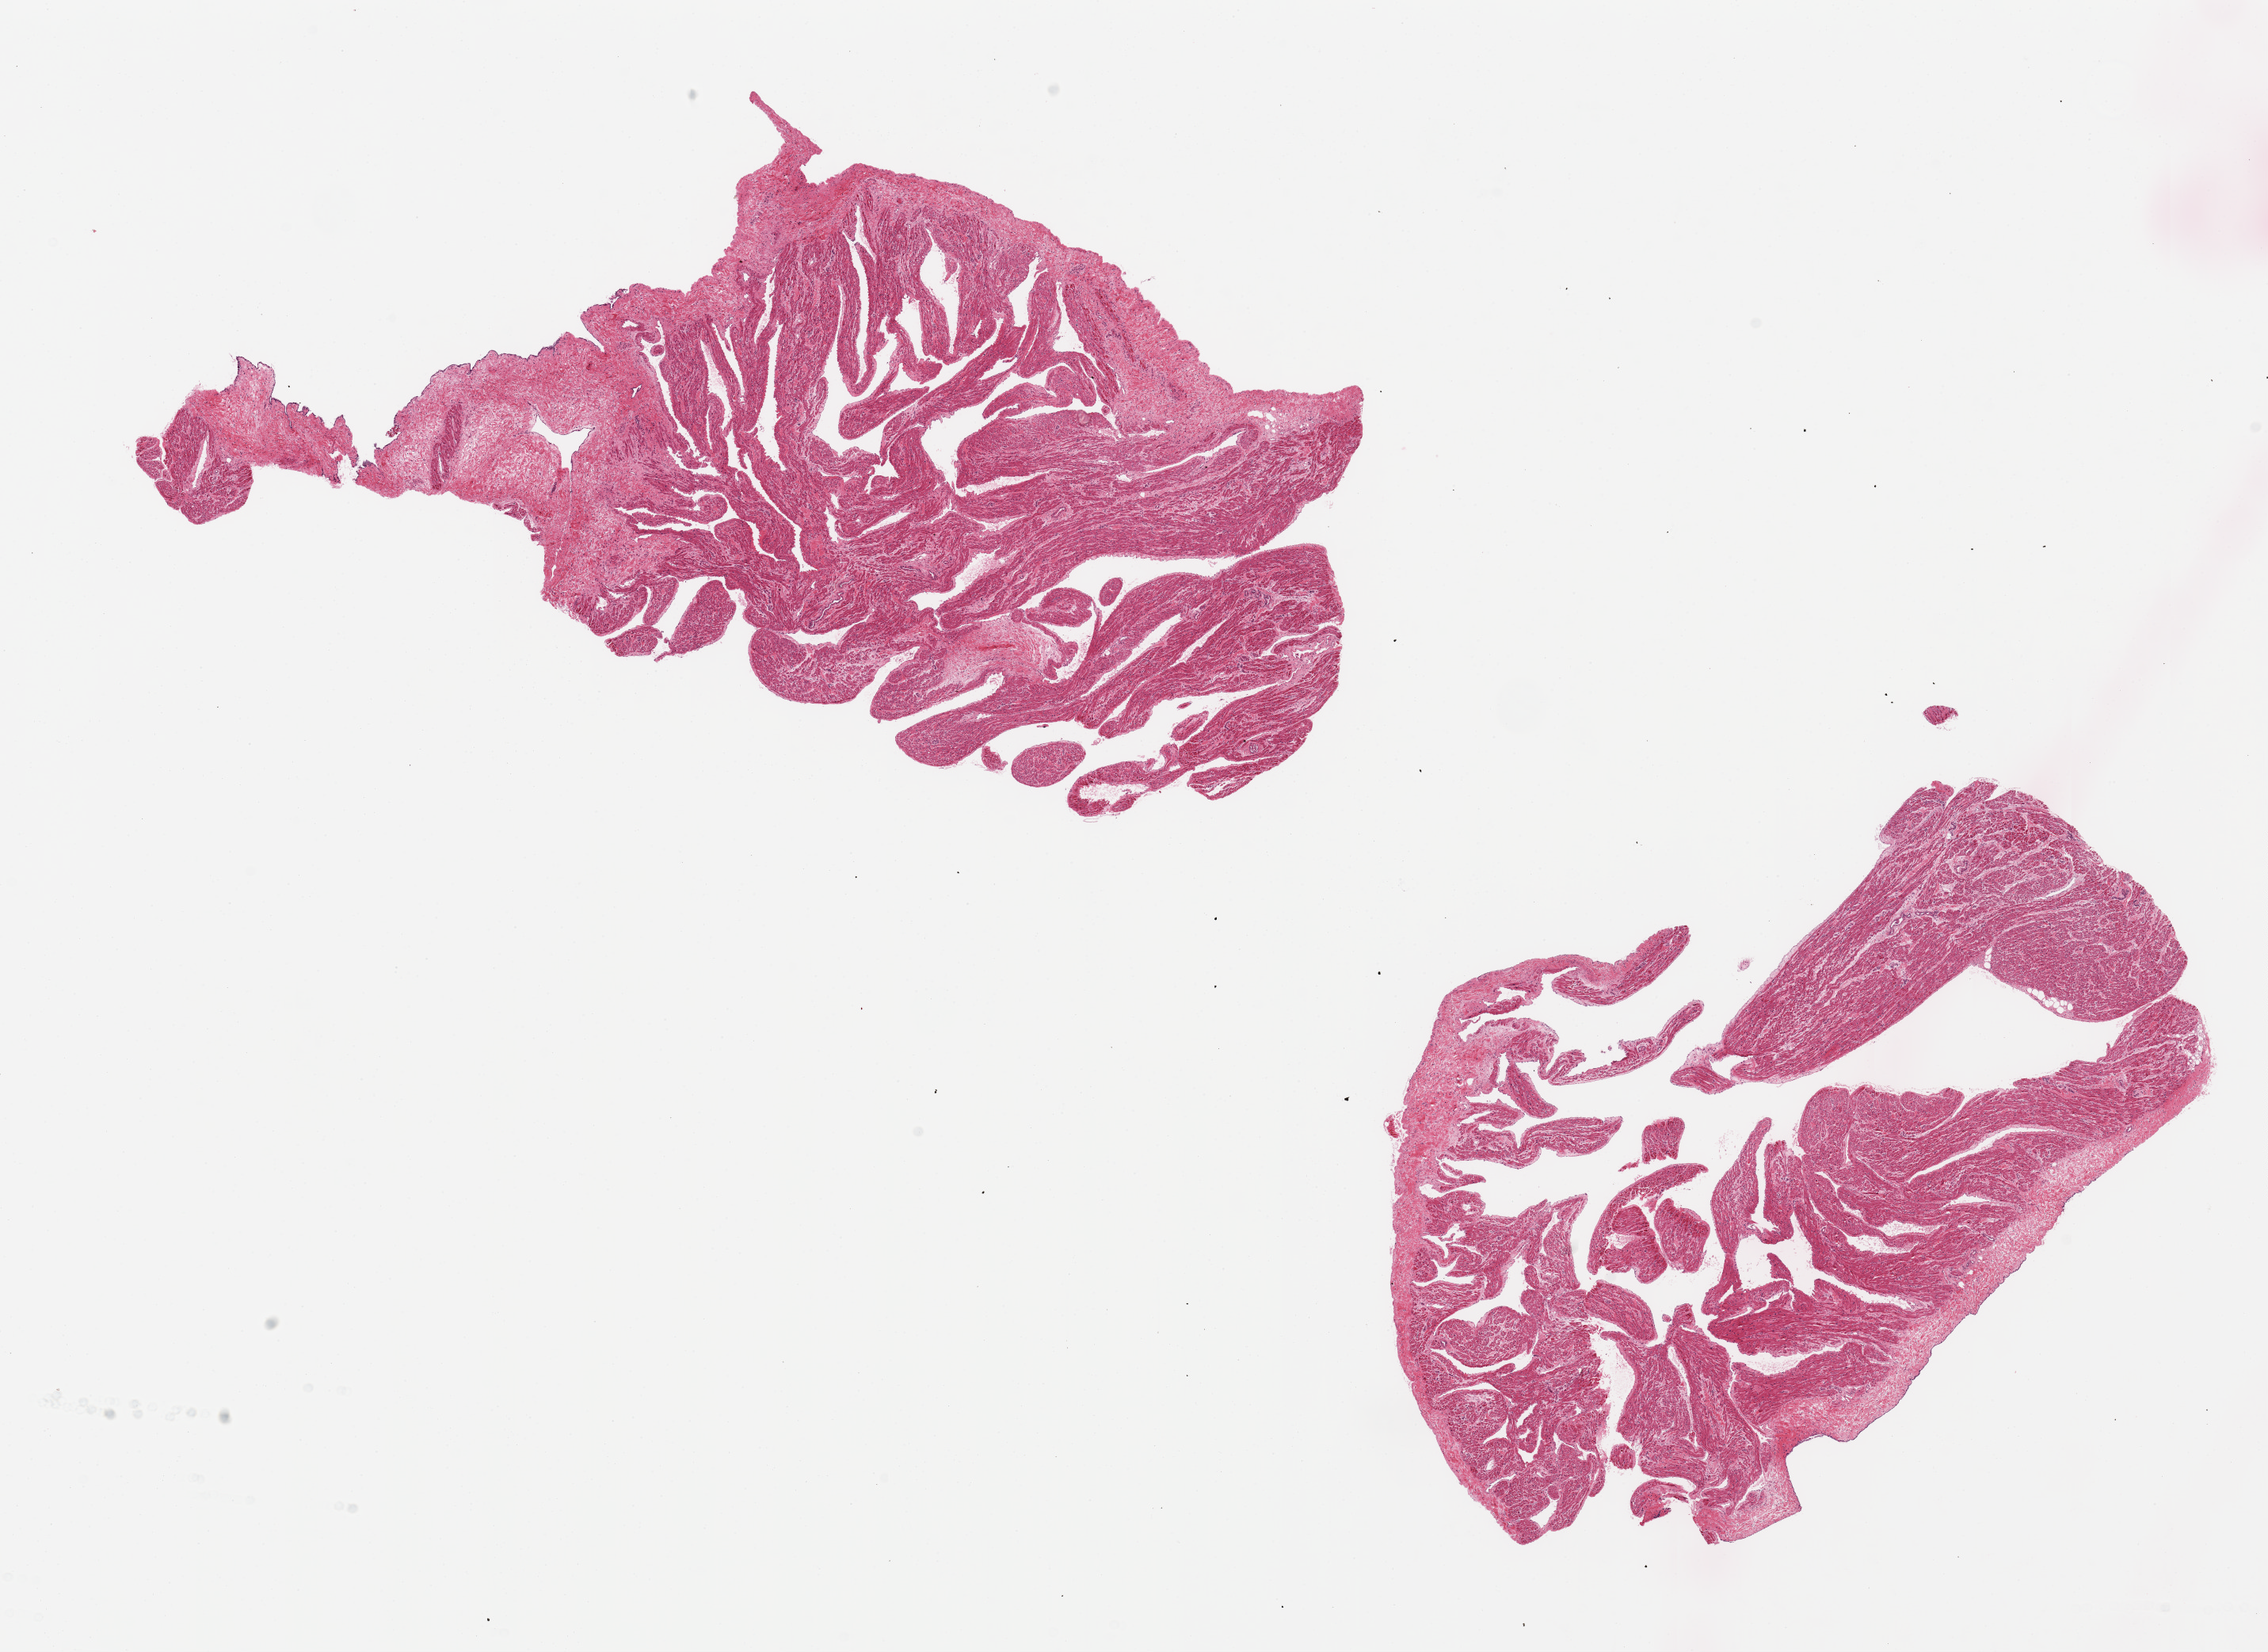
Hematoxylin and eosin (H&E) whole-slide image, brightfield — whole scanned area (about 22.6 x 16.5 mm) shown as a low-resolution overview, PAXgene-fixed paraffin-embedded (PFPE) section, section of auricular appendage (target tissue), donor tissue sample.
Pathologist's review note for this sample: 2 pieces; fibromuscular tissue with mesothelial lining.